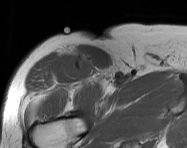
MRI of an extremity soft-tissue mass, one axial slice. Position 113 of 114 along the scan axis. MR volume resampled by the dataset authors to the PET/CT grid (not the native acquisition matrix). 3.27 mm slice thickness. 187 × 148 image matrix. Male patient. Case-level facts recorded for this patient, not image findings: histological type: pleiomorphic leiomyosarcoma; grade: intermediate; site of the primary tumour: right thigh.
Outlined on this slice (expert contour drawn on MRI and transferred to this co-registered scan by the dataset authors):
- gross tumour volume including surrounding oedema: bounding box <79,59,92,73> (left, top, right, bottom; pixels)